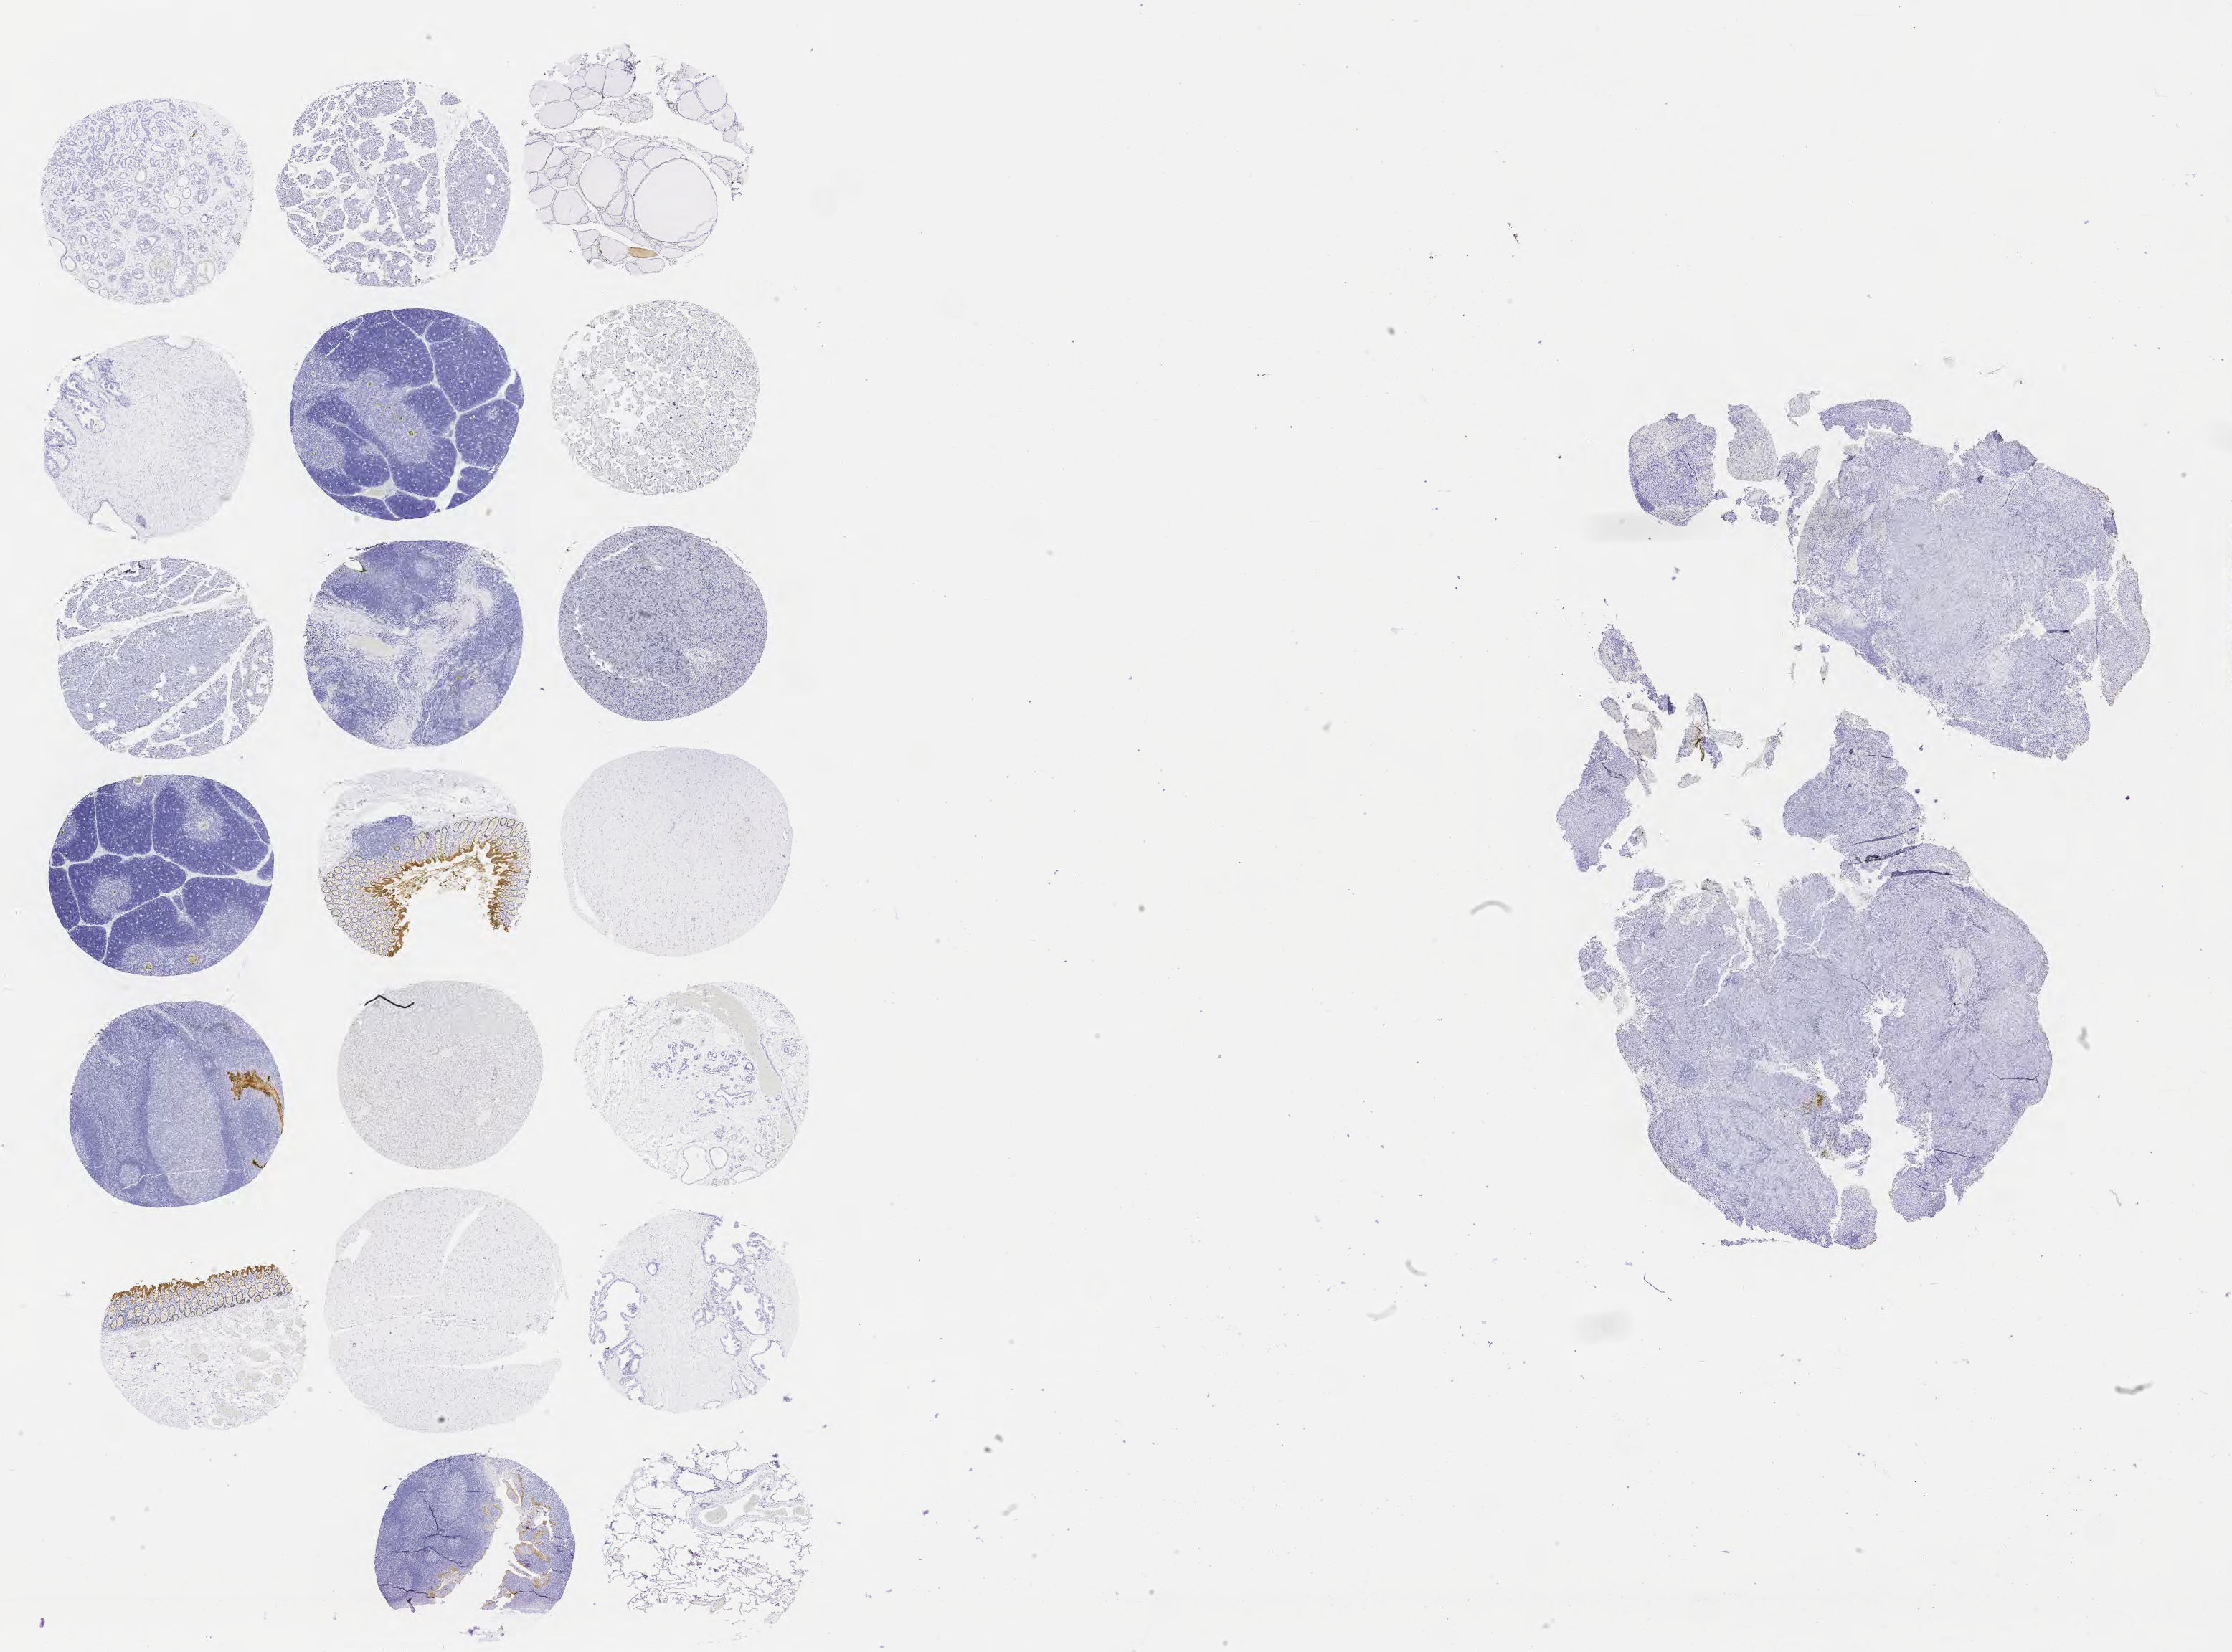
Immunohistochemistry (IHC) whole-slide image stained for carcinoembryonic antigen (CEA), low-resolution overview of the scanned area, about 25.2 x 18.6 mm. Specimen: tumor tissue. Site: cervix. Female patient, 70 years old.
Histologic diagnosis: Squamous cell carcinoma, large cell, nonkeratinizing, NOS.